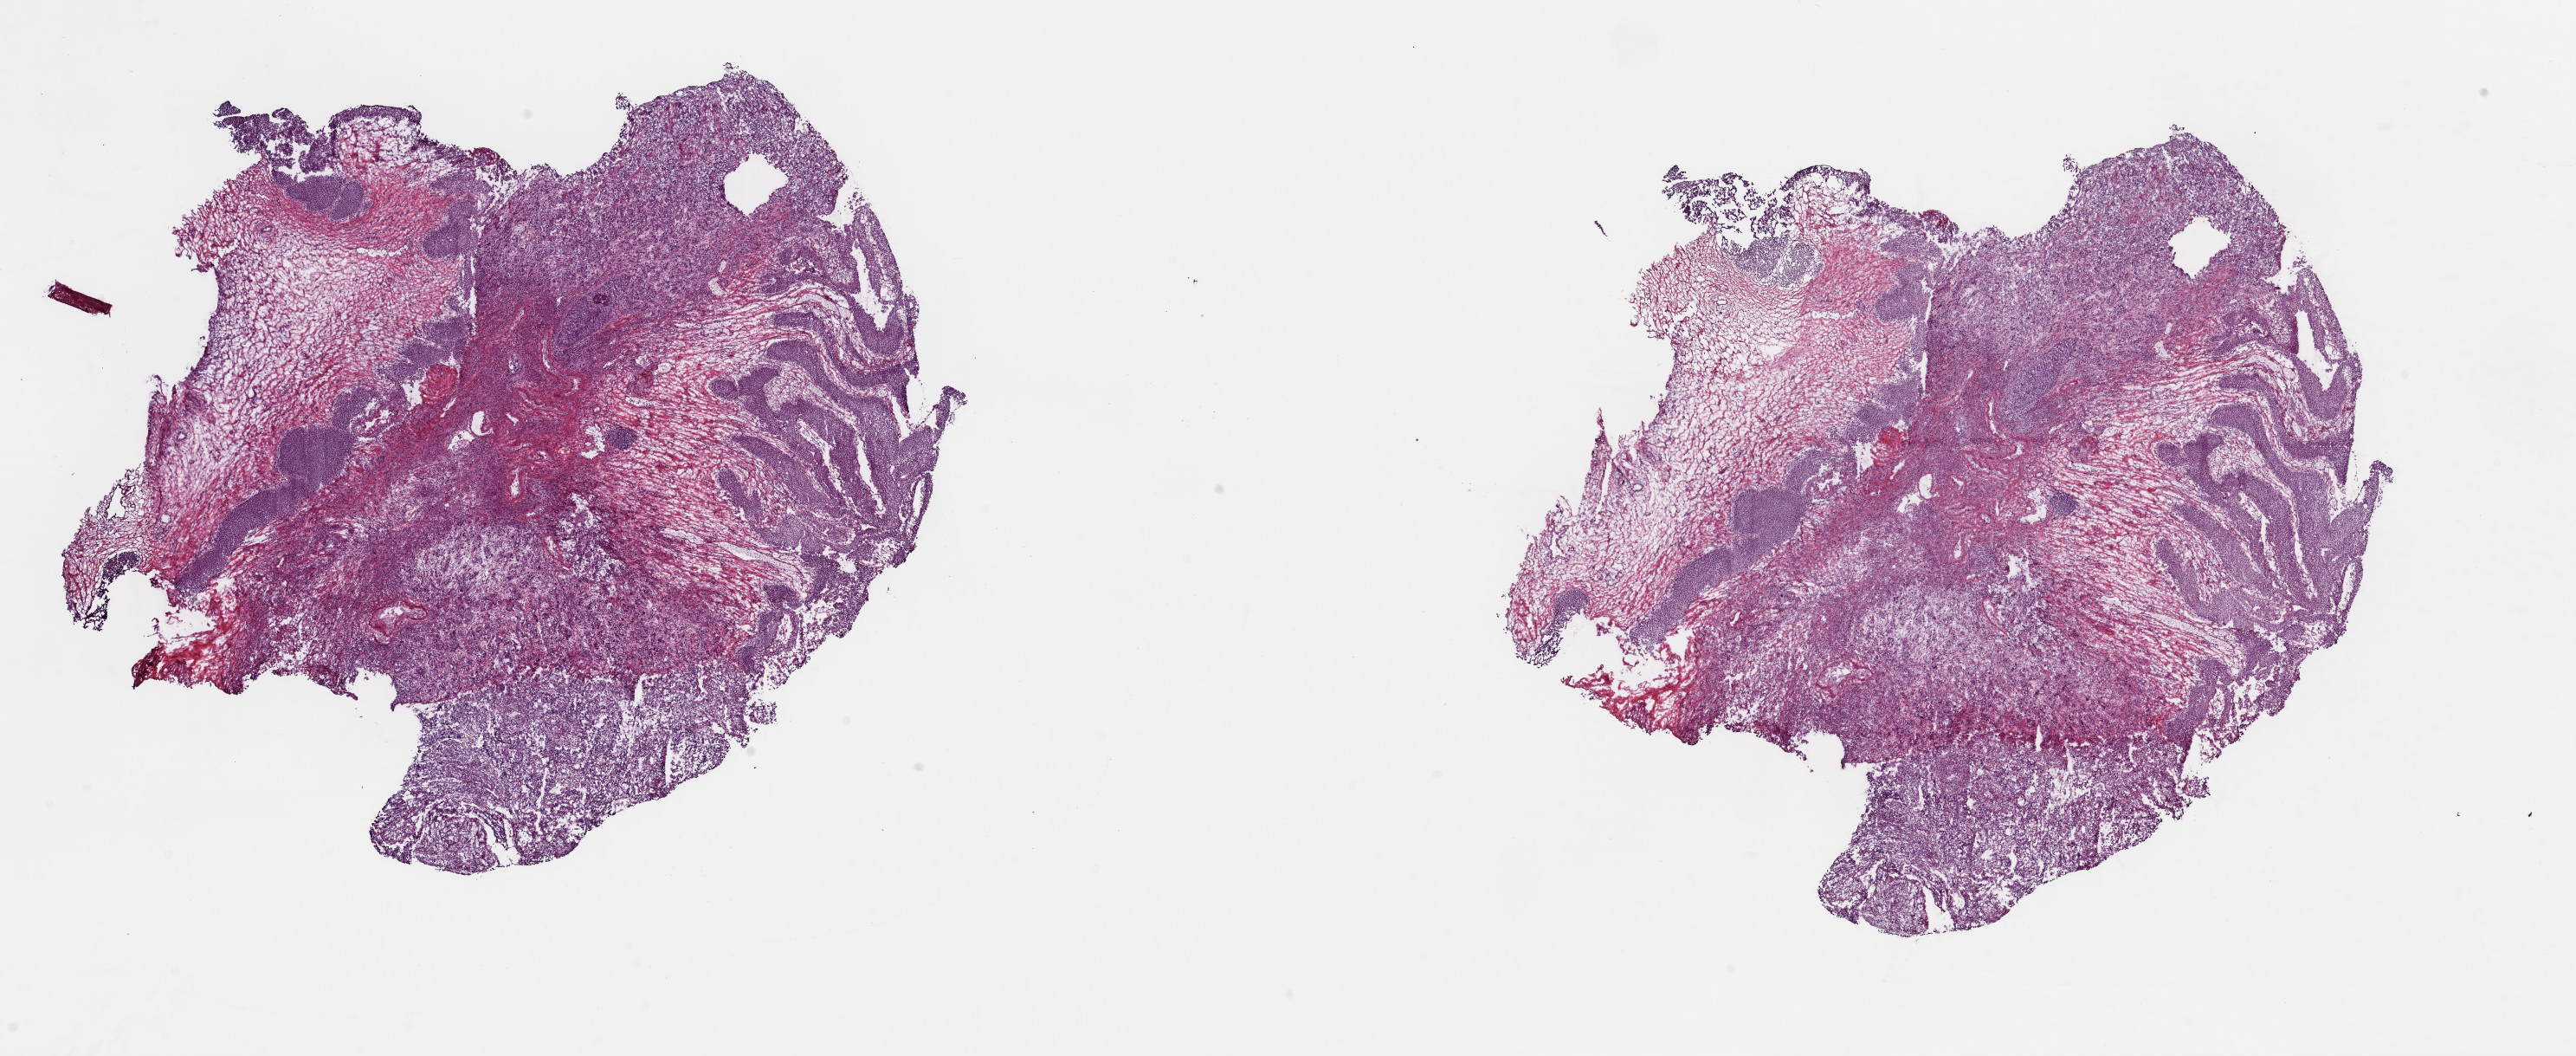
Hematoxylin and eosin (H&E) stained whole-slide image, shown as a low-resolution overview of the whole scanned area (about 23.5 x 9.6 mm). Frozen section from the top of the tissue portion. Primary tumour sample from the bladder. Male patient; age at initial diagnosis 56 years. Histologic grade: high grade. Composition of this section per pathologist review: tumour cells 45%, tumour nuclei 65%, normal cells 4%, stromal cells 46%, necrosis 5%. Inflammatory infiltration, as recorded: lymphocyte infiltration 25%, monocyte infiltration 0%, neutrophil infiltration 5%.
AJCC pathologic stage: III (6th edition). Diagnosis: Transitional cell carcinoma. Lymph nodes positive (case pathology): 0 of 5 examined.